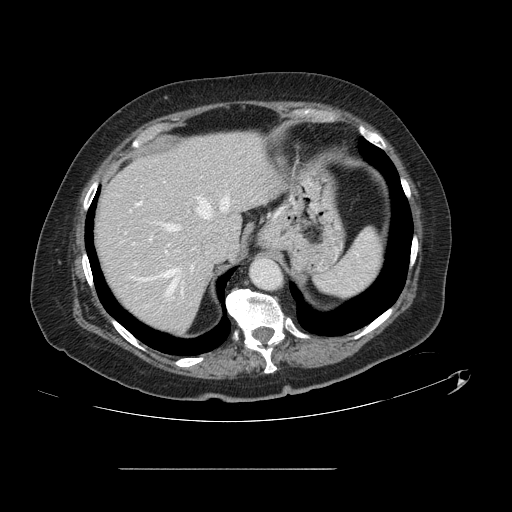
Contrast-enhanced abdominal CT, one axial slice; position 107 of 148 along the scan axis; 120 kVp; soft-tissue window (W 400 / L 40 HU); 2.5 mm slice thickness; 512 × 512 image matrix, field of view 439 × 439 mm. Female patient, age 75 years. Case-level facts recorded for this patient, not image findings: diagnosis: colorectal cancer liver metastases, imaged before liver resection; multiple liver metastases: no; largest metastasis: 2.4 cm; disease in both lobes: no.
Outlined on this slice (outlined manually by an expert reader):
- hepatic veins: box from (x=140, y=194) to (x=230, y=295) px
- liver: (x=94, y=132)–(x=278, y=332)
- planned liver remnant (the part of the liver to remain after resection): (x=94, y=132)–(x=278, y=332)
- portal vein (with intrahepatic branches): (x=138, y=203)–(x=141, y=205)